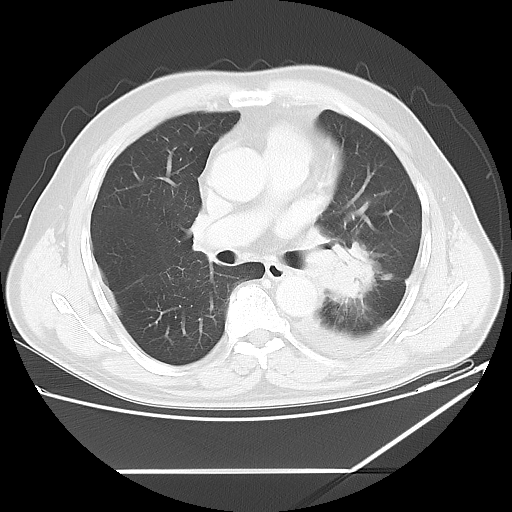
Chest CT, one axial slice; position 33 of 60 along the scan axis; reconstruction kernel LUNG; 120 kVp; lung window (W 1500 / L -600 HU); 5 mm slice thickness; 512 × 512 image matrix. Male patient, age 62 years. From the clinical record (not read from this slice): clinical TNM (as recorded): T3 N0 M1.
Structures marked on this image (rectangle marked by the reading radiologist):
- lung tumour (recorded histology: adenocarcinoma): bounding box [x1, y1, x2, y2] px = [325, 236, 385, 306]
- lung tumour (recorded histology: adenocarcinoma): [326, 236, 384, 306]